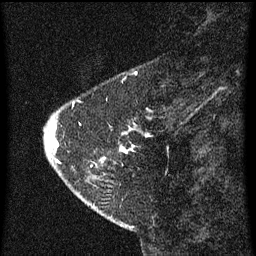
Breast MRI (dynamic contrast-enhanced), one sagittal slice. Dynamic contrast-enhanced series, image 2 of 3 at this slice position (ordered by acquisition). 1.5 T. TE 4.2 ms, TR 8 ms. 2 mm slice thickness. 256 × 256 image matrix, field of view 180 × 180 mm. Female patient, age 47 years.
Structures marked on this image (semi-automatically segmented with operator editing):
- analysis volume of interest (the breast-tissue region the enhancement analysis was run in; not a lesion): box from (x=44, y=100) to (x=151, y=199) px
- tumour enhancement mask (voxels above the 70 % enhancement threshold inside the analysis volume of interest): (x=54, y=102)–(x=149, y=163)